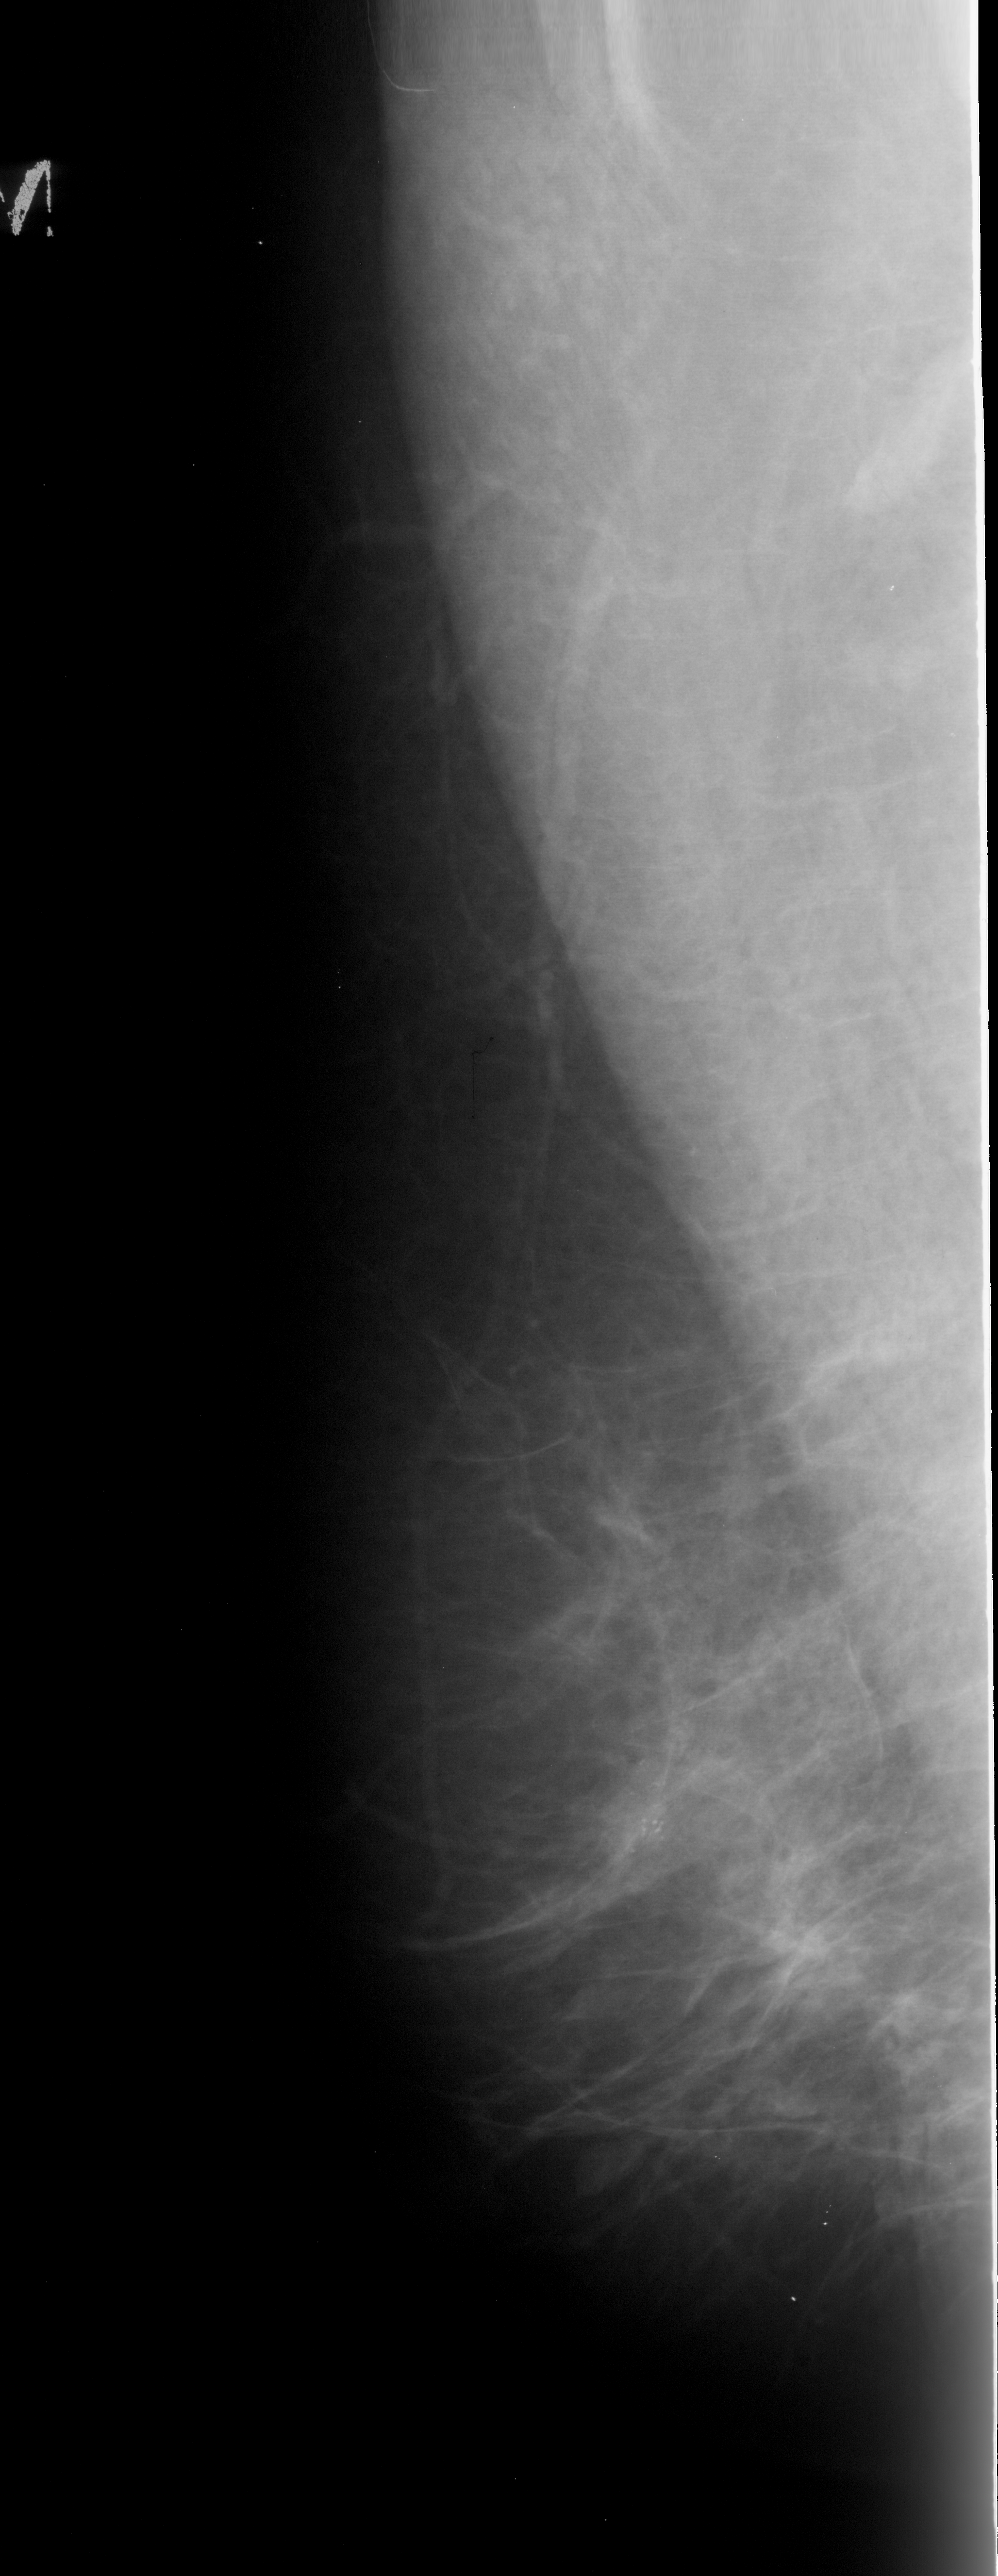
Digitized screen-film mammogram, left breast, MLO view, BI-RADS breast density category 2 (scale 1–4).
- Marked findings (only marked abnormalities are described; nothing is implied about the rest of the image): calcifications, morphology pleomorphic, distribution clustered; BI-RADS assessment category 4; pathology result (as recorded, not read from the image): malignant.